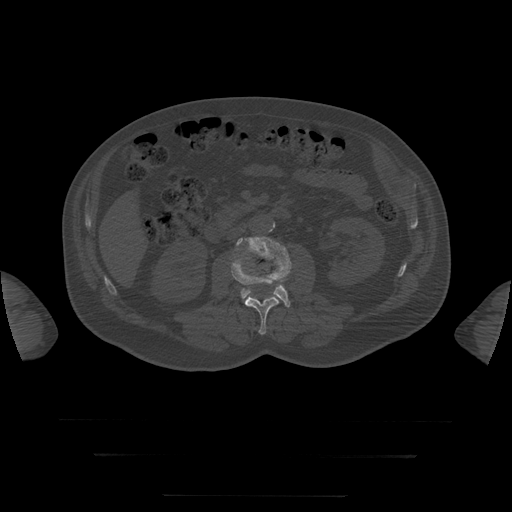
CT including the spine, one axial slice; slice 13 of 397 in the series (ordered by position); reconstruction kernel STANDARD; 120 kVp; bone window (W 1800 / L 400 HU); 1.25 mm slice thickness; 512 × 512 image matrix, field of view 510 × 510 mm. Patient age 73 years. Case-level facts recorded for this patient, not image findings: primary cancer: prostate.
Annotated regions visible in this slice (semi-automatic segmentation, software-assisted and operator-edited):
- L3 vertebra: box from (x=236, y=236) to (x=292, y=307) px